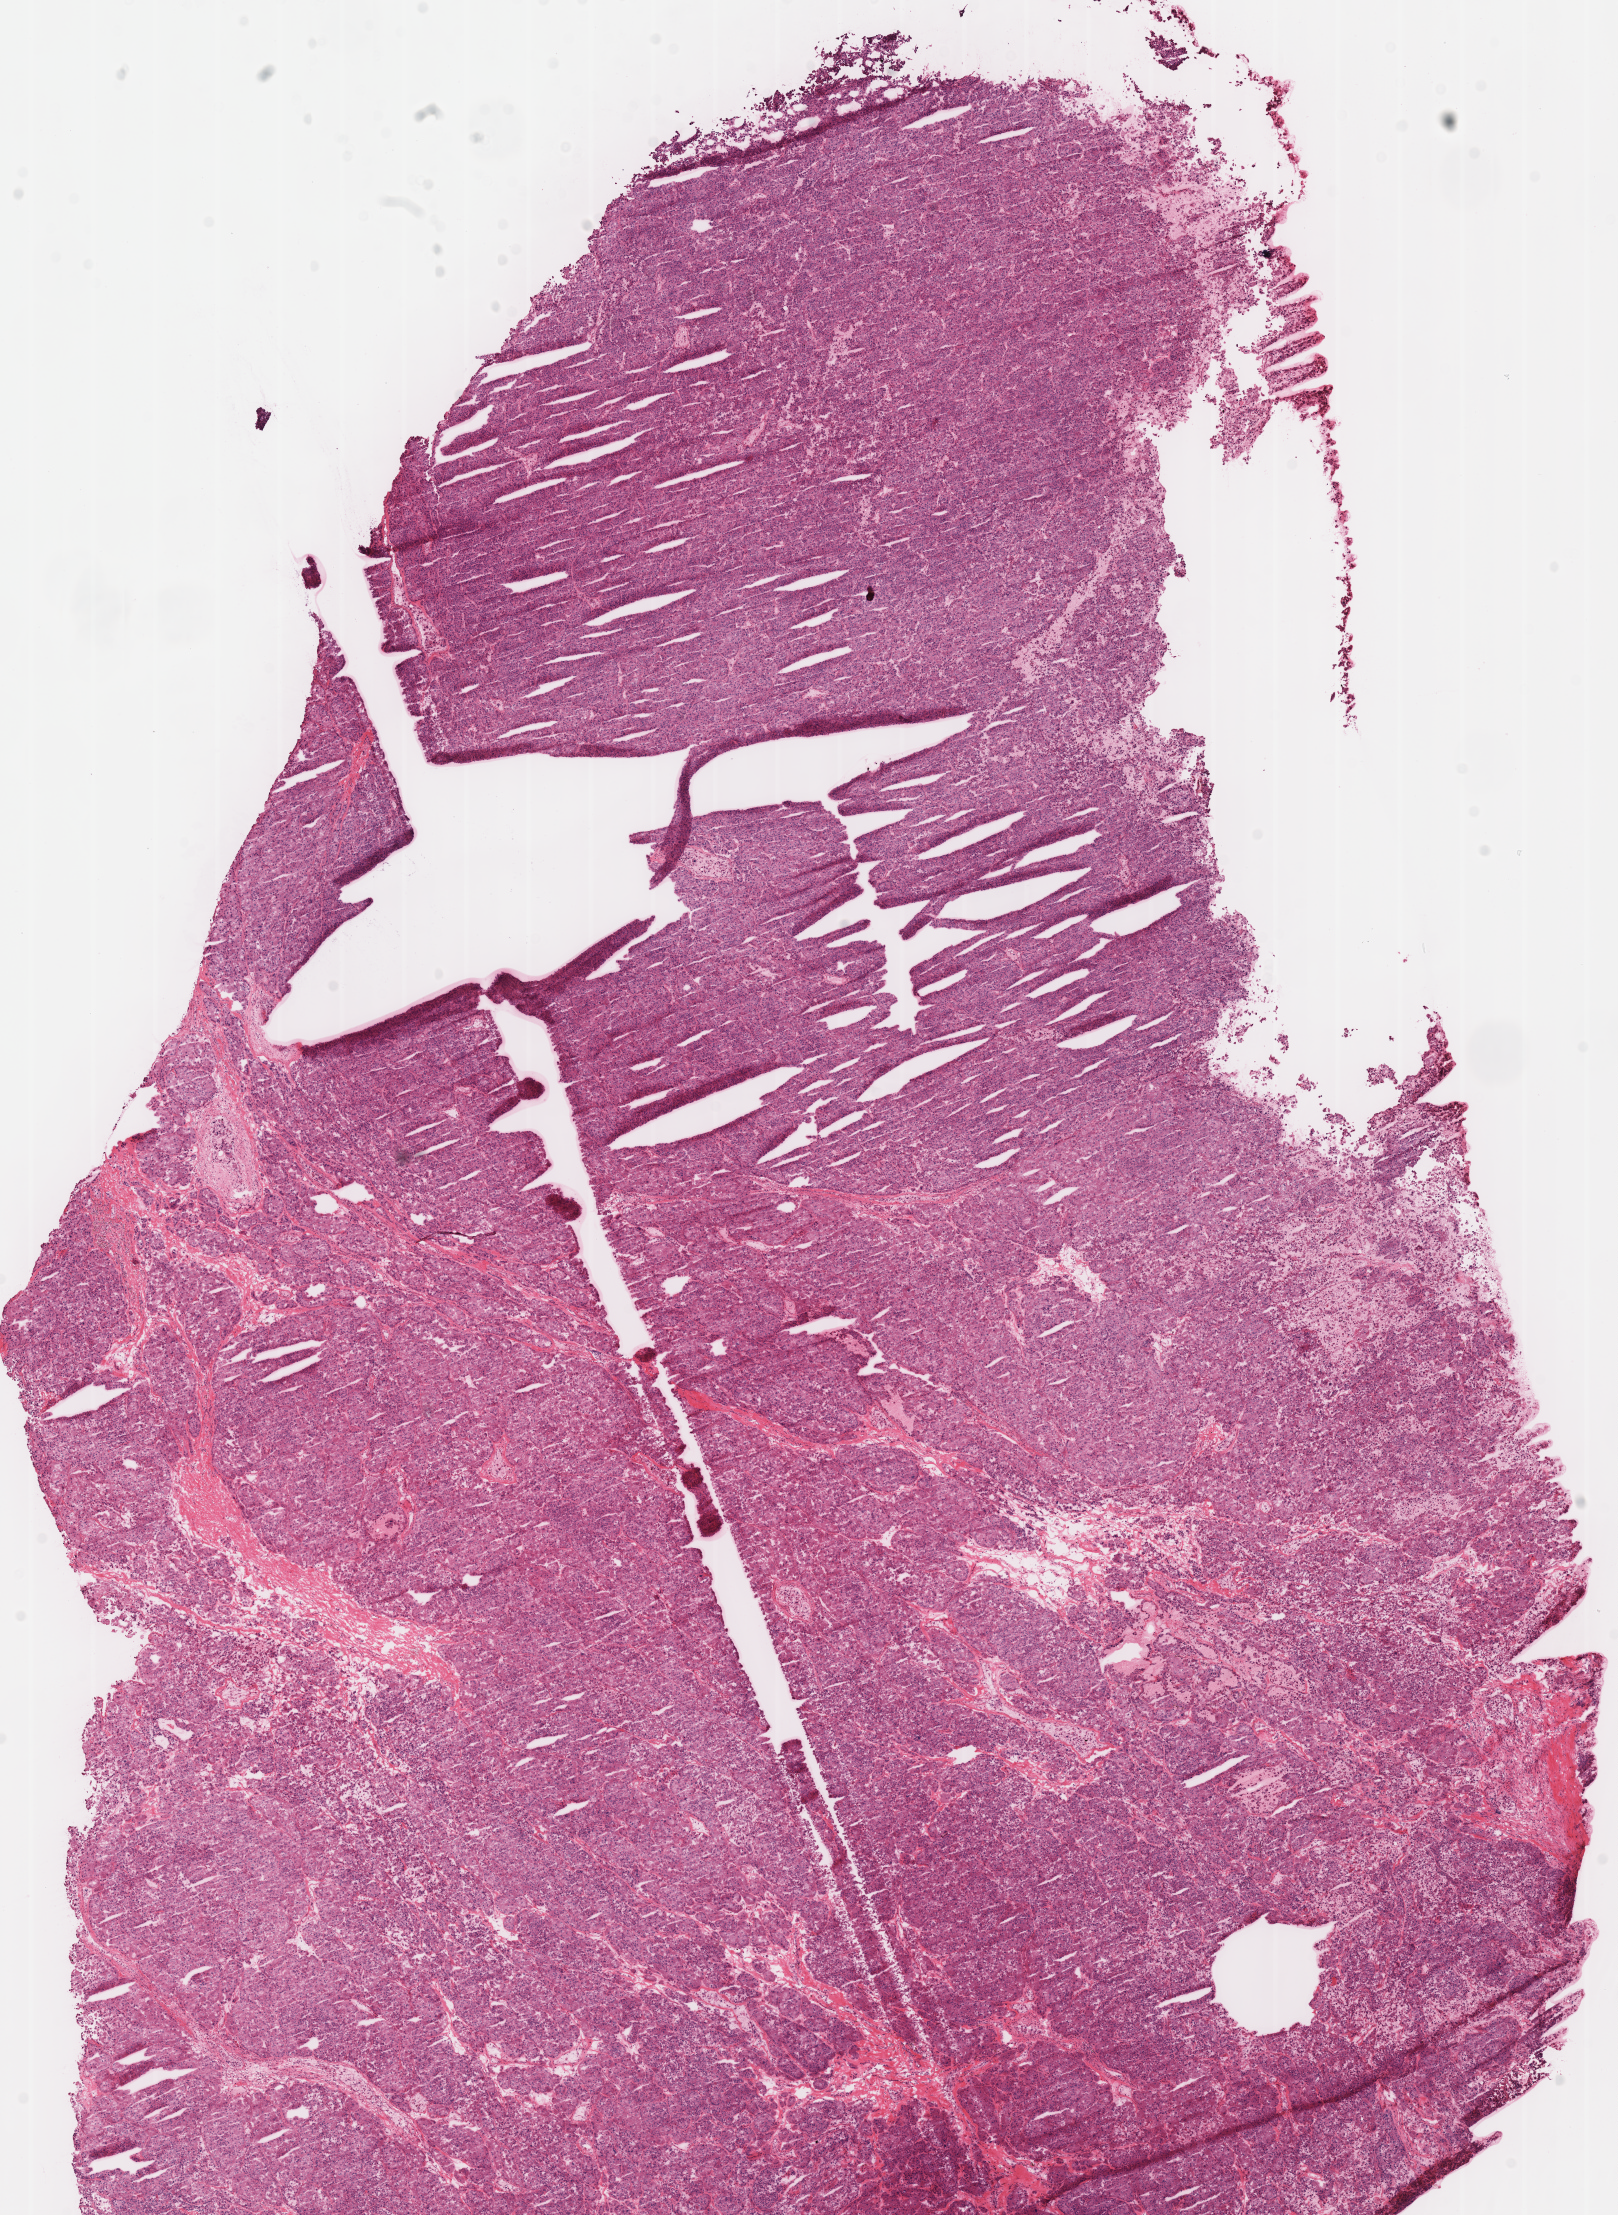
Whole-slide histology image, H&E-stained, a low-resolution overview of the entire scanned area, about 12.7 x 17.4 mm. Frozen section from the top of the tissue portion. Sample: primary tumour, kidney. Patient: male, age at initial diagnosis 67 years. Slide review estimates, as recorded: tumour cells 90%, tumour nuclei 90%, normal cells 0%, stromal cells 10%, necrosis 0%.
• lymph nodes positive (case pathology): 1 of 33 examined
• laterality: left
• AJCC pathologic stage: IV (6th edition)
• diagnosis: Renal cell carcinoma, chromophobe type